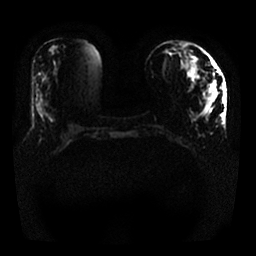
Breast MRI, one axial slice; slice 5 of 25 in the series (ordered by position); diffusion-weighted series; image 2 of 4 stored at this slice position (different b-values; order by instance number); 1.5 T; 4 mm slice thickness; 256 × 256 image matrix. Female patient.
Structures marked on this image (manually delineated by an expert):
- tumour on diffusion-weighted imaging: bounding box <206,80,217,115> (left, top, right, bottom; pixels)